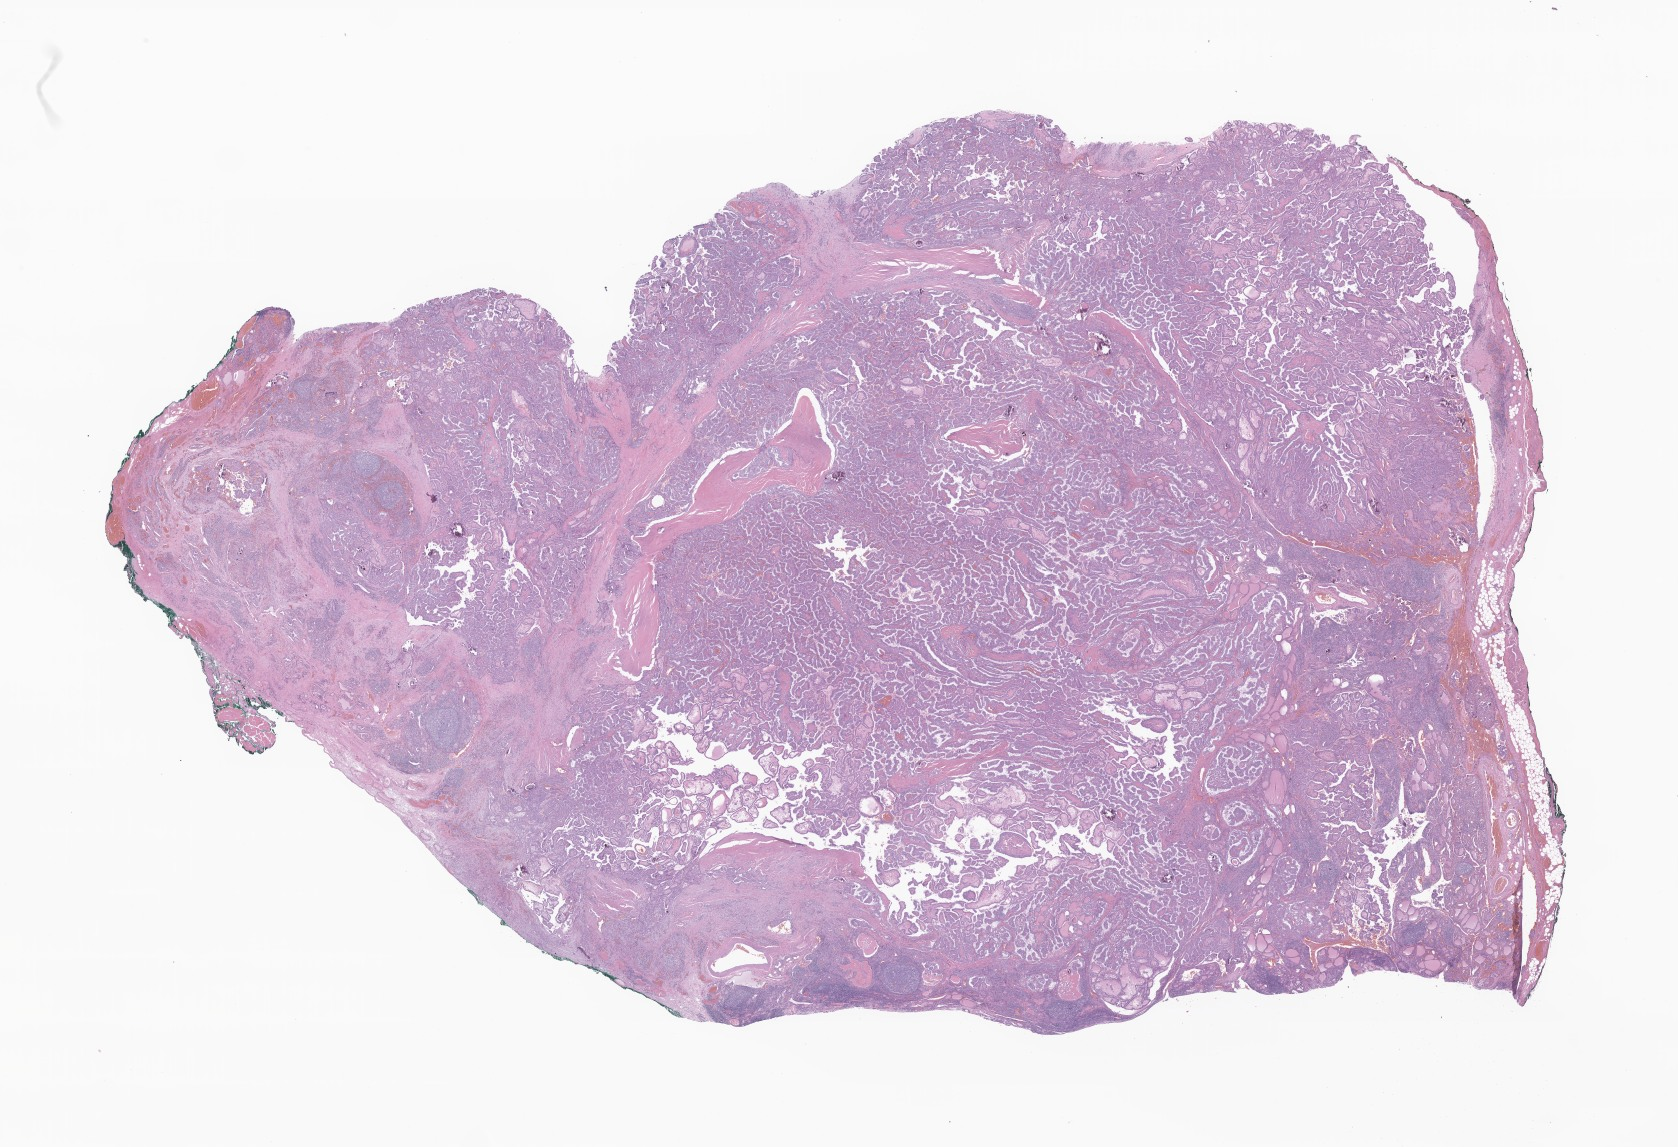
H&E whole-slide image of tumor tissue from the thyroid, a low-resolution overview of the entire scanned area, about 28.3 x 19.3 mm; formalin-fixed, paraffin-embedded (FFPE) tissue. Patient female; age 207 months (17 years 3 months).
Diagnosis (ICD-O-3 morphology term): Papillary carcinoma, NOS.